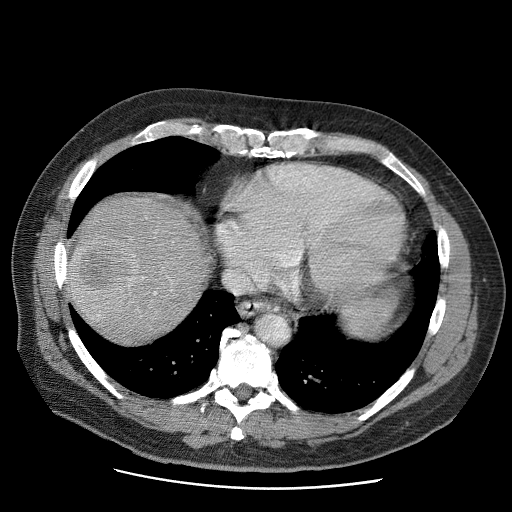
Contrast-enhanced abdominal CT (liver protocol), one axial slice. Soft-tissue window (W 400 / L 40 HU). 512 × 512 image matrix. From the clinical record (not read from this slice): diagnosis: hepatocellular carcinoma (patient treated with transarterial chemoembolisation; whether this scan precedes or follows treatment is not stated here); TNM stage (as recorded): Stage-IIIA; Child-Pugh class: A; tumour differentiation: moderately differentiated; tumour nodularity: multinodular.
Annotated regions visible in this slice (semi-automatic segmentation, software-assisted and operator-edited):
- liver parenchyma outside the tumour (the mass and vessels are separate outlines, so this box may not span the whole liver): bounding box (x1, y1, x2, y2) in pixels: (67, 194, 208, 342)
- mass: (67, 230, 139, 319)
- liver vessels: (154, 292, 157, 295)